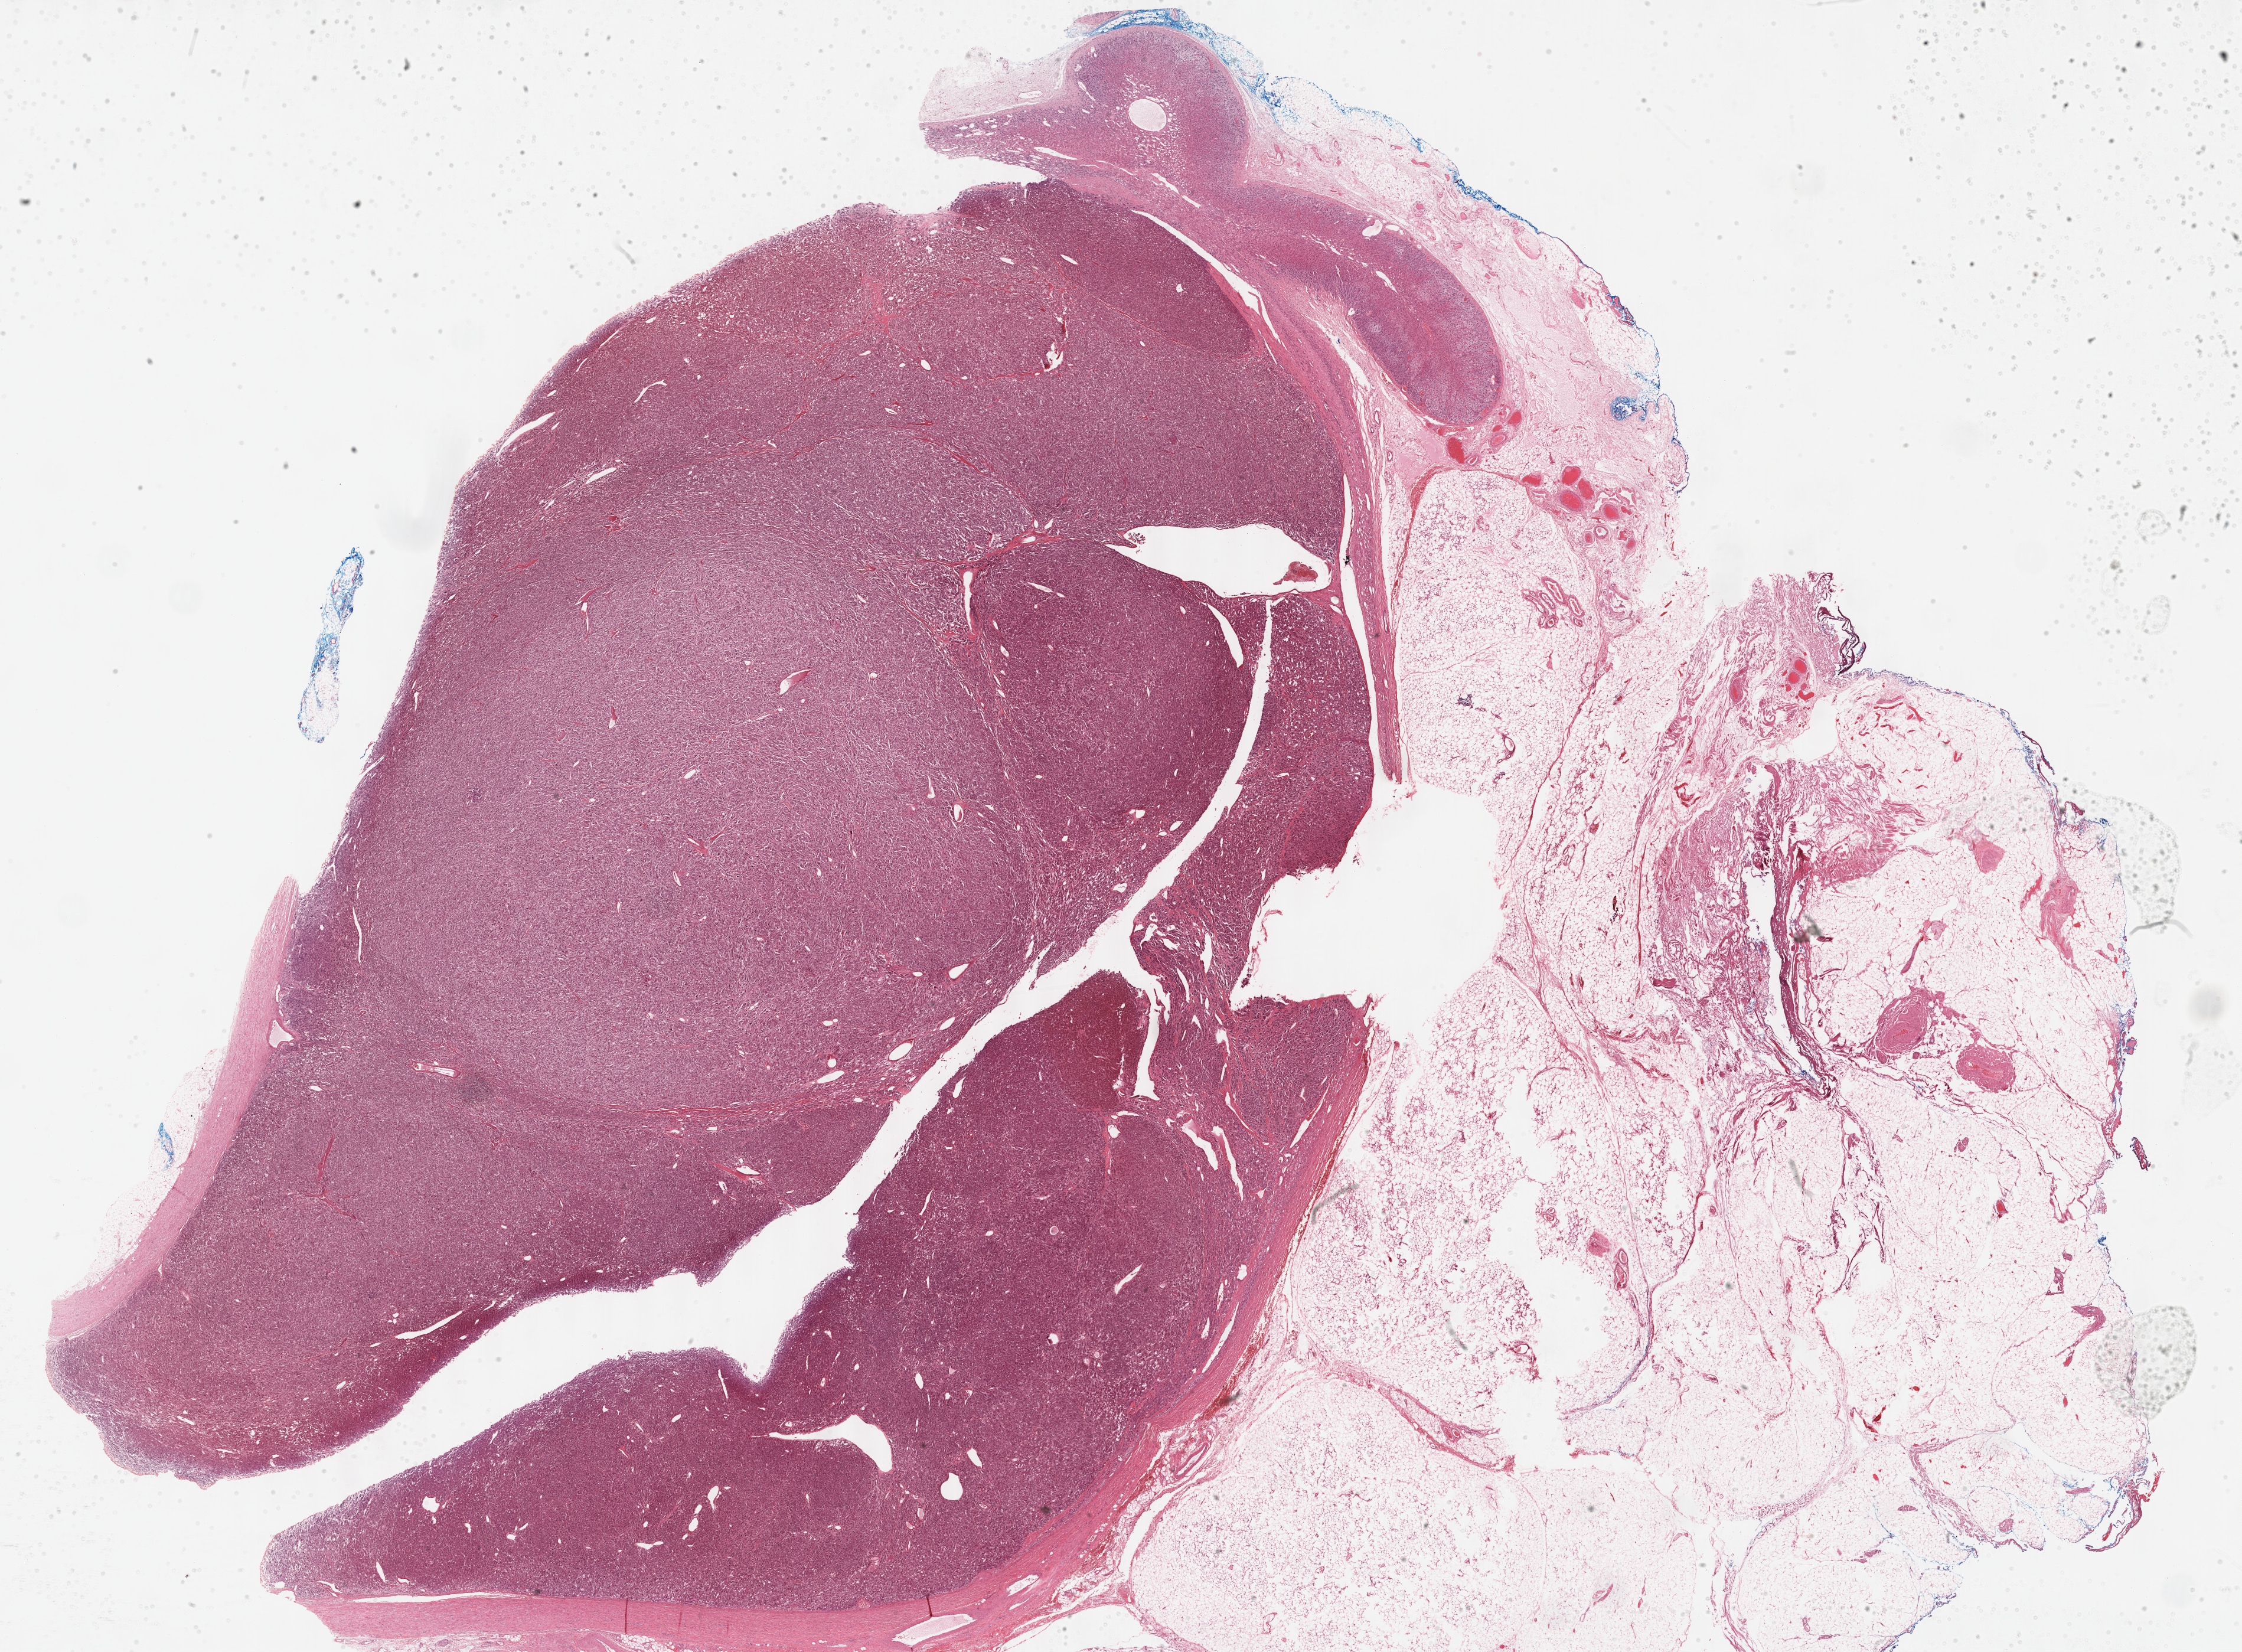
Digitized H&E-stained tissue section (whole slide), shown as a low-resolution overview of the whole scanned area (about 30.7 x 22.6 mm, from a 40x scan); formalin-fixed paraffin-embedded (FFPE) diagnostic section; primary tumour sample from the adrenal gland. Patient: female, age at initial diagnosis 31 years.
Diagnosis: Pheochromocytoma, NOS.